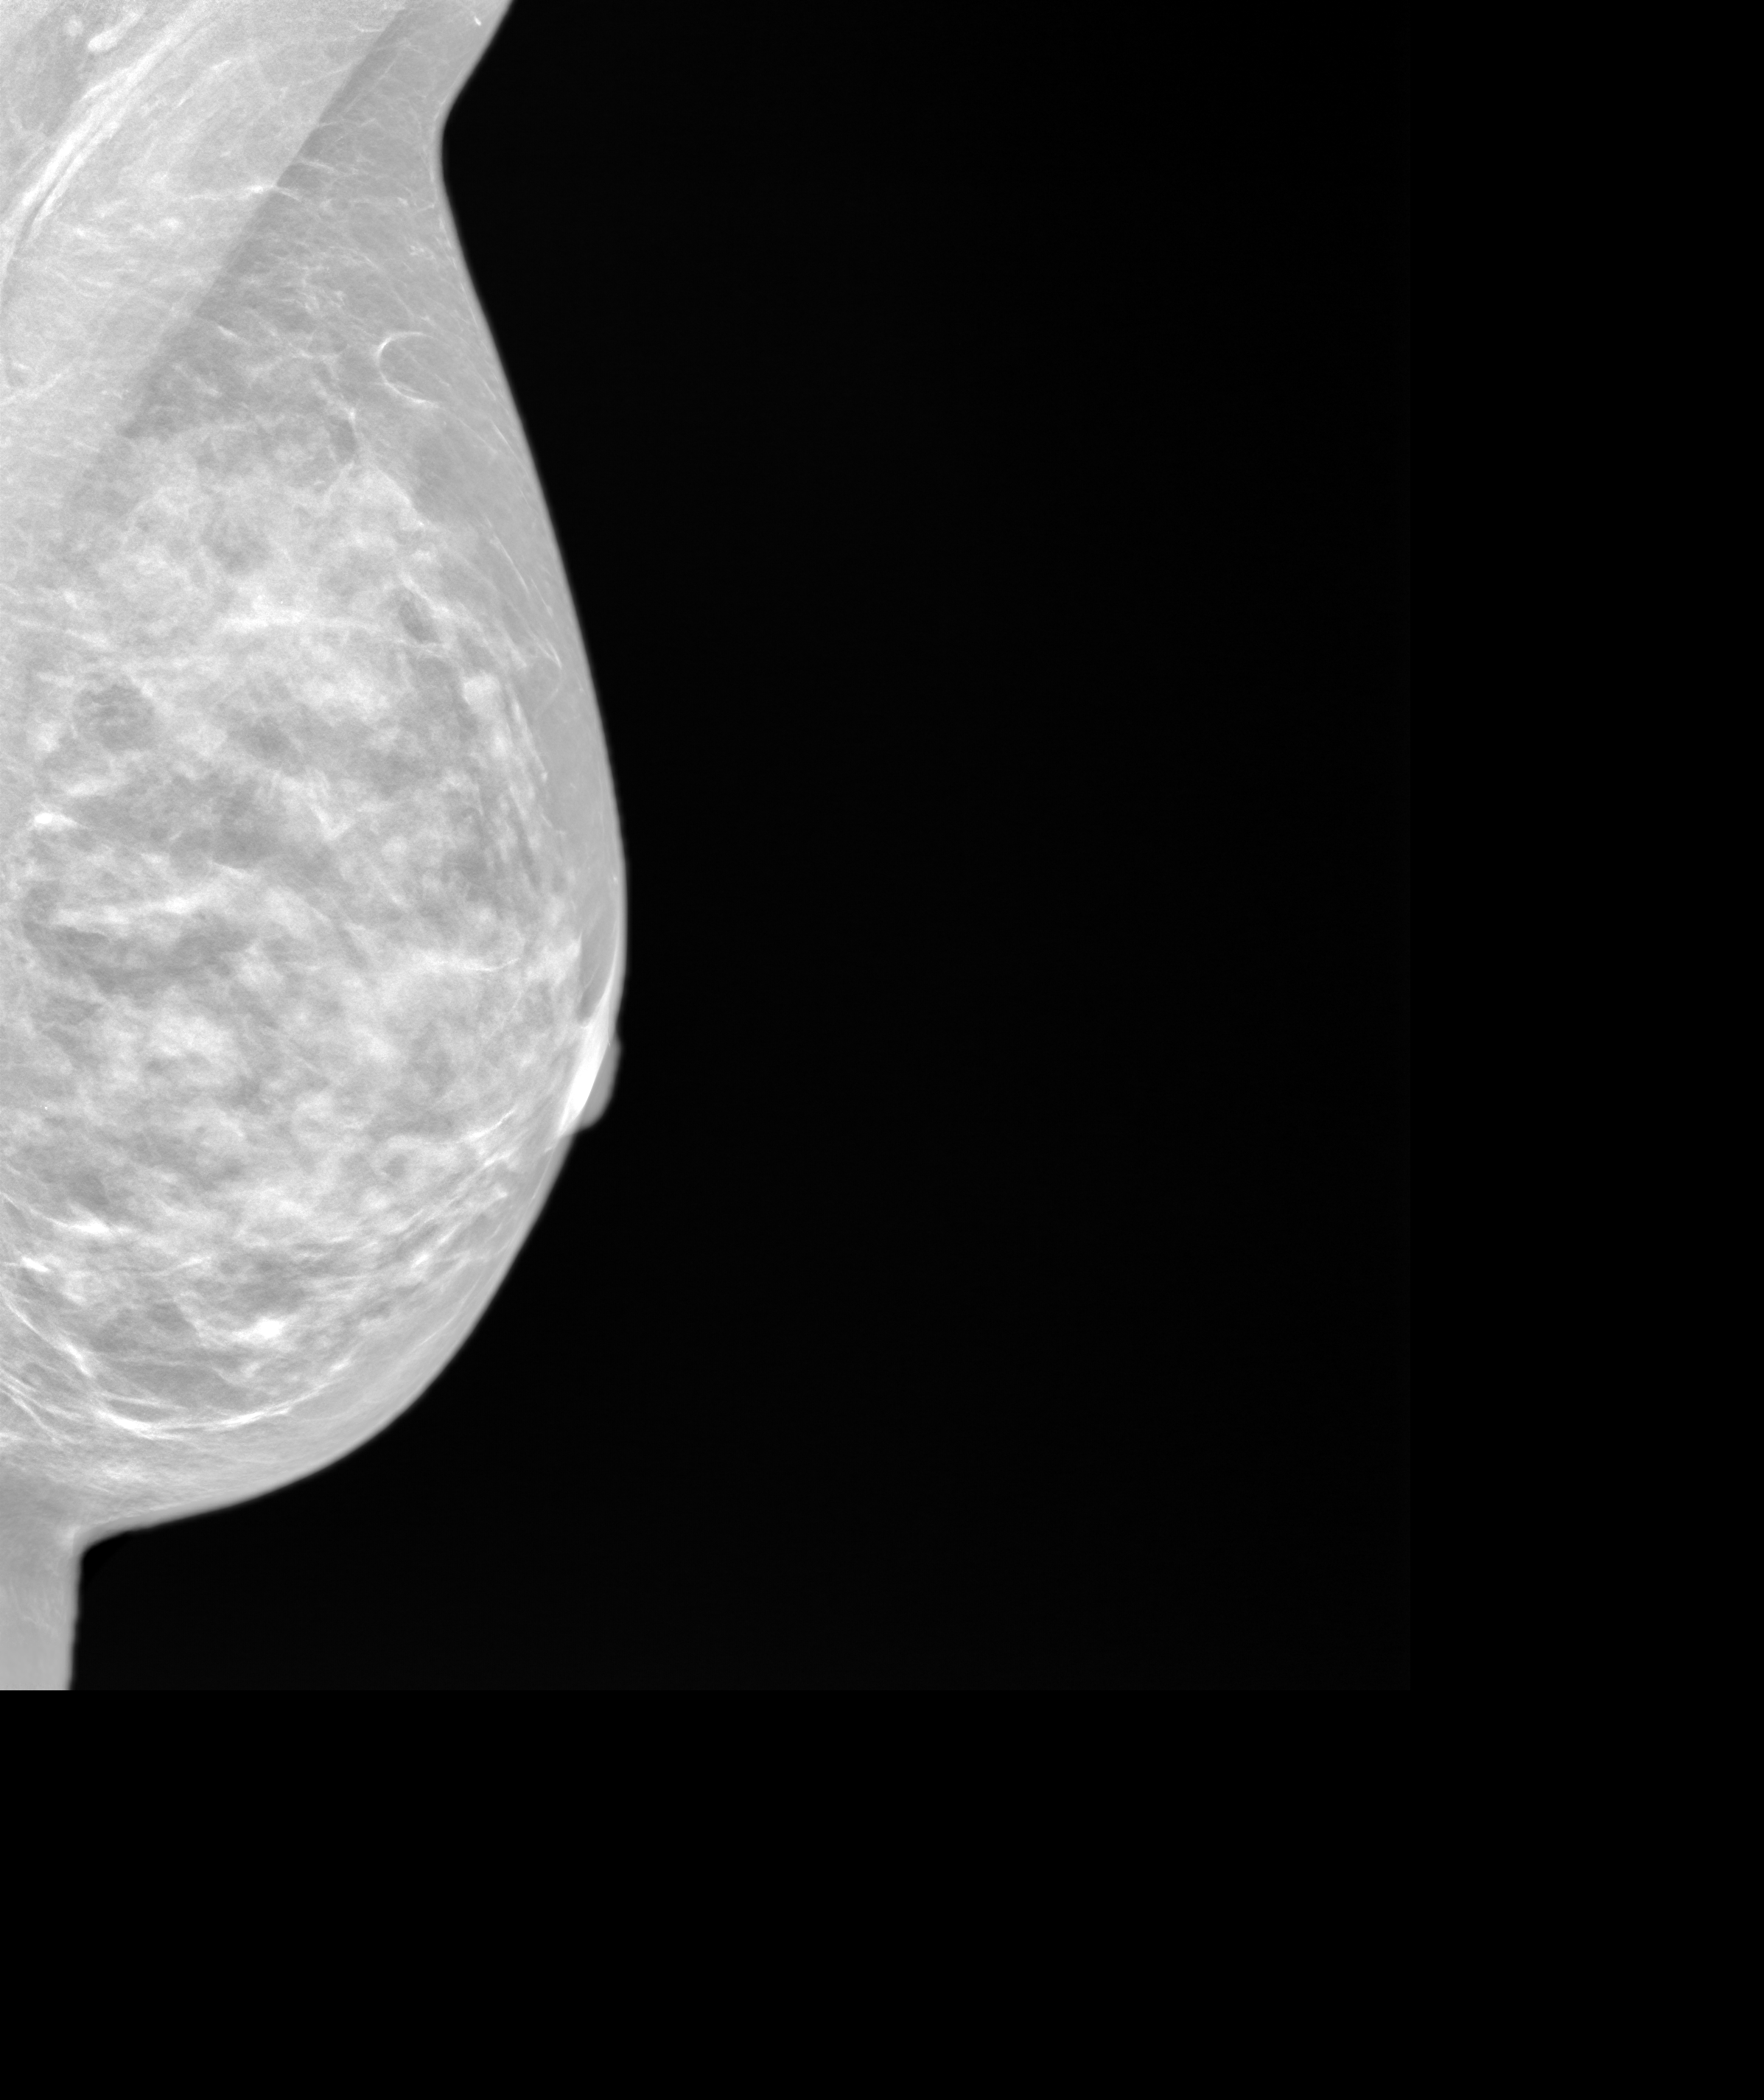
Synthesized 2-D mammogram reconstructed from digital breast tomosynthesis, left breast, MLO view, annual screening mammography examination, system: SenoIris_1SP1.2(425). Female patient, age 73 years.
- breast density at the screening exam (both breasts): extremely dense (BI-RADS density category d)
- final BI-RADS assessment for this screening round (tomosynthesis exam, both breasts): category 1
- recall: no recall after this screen